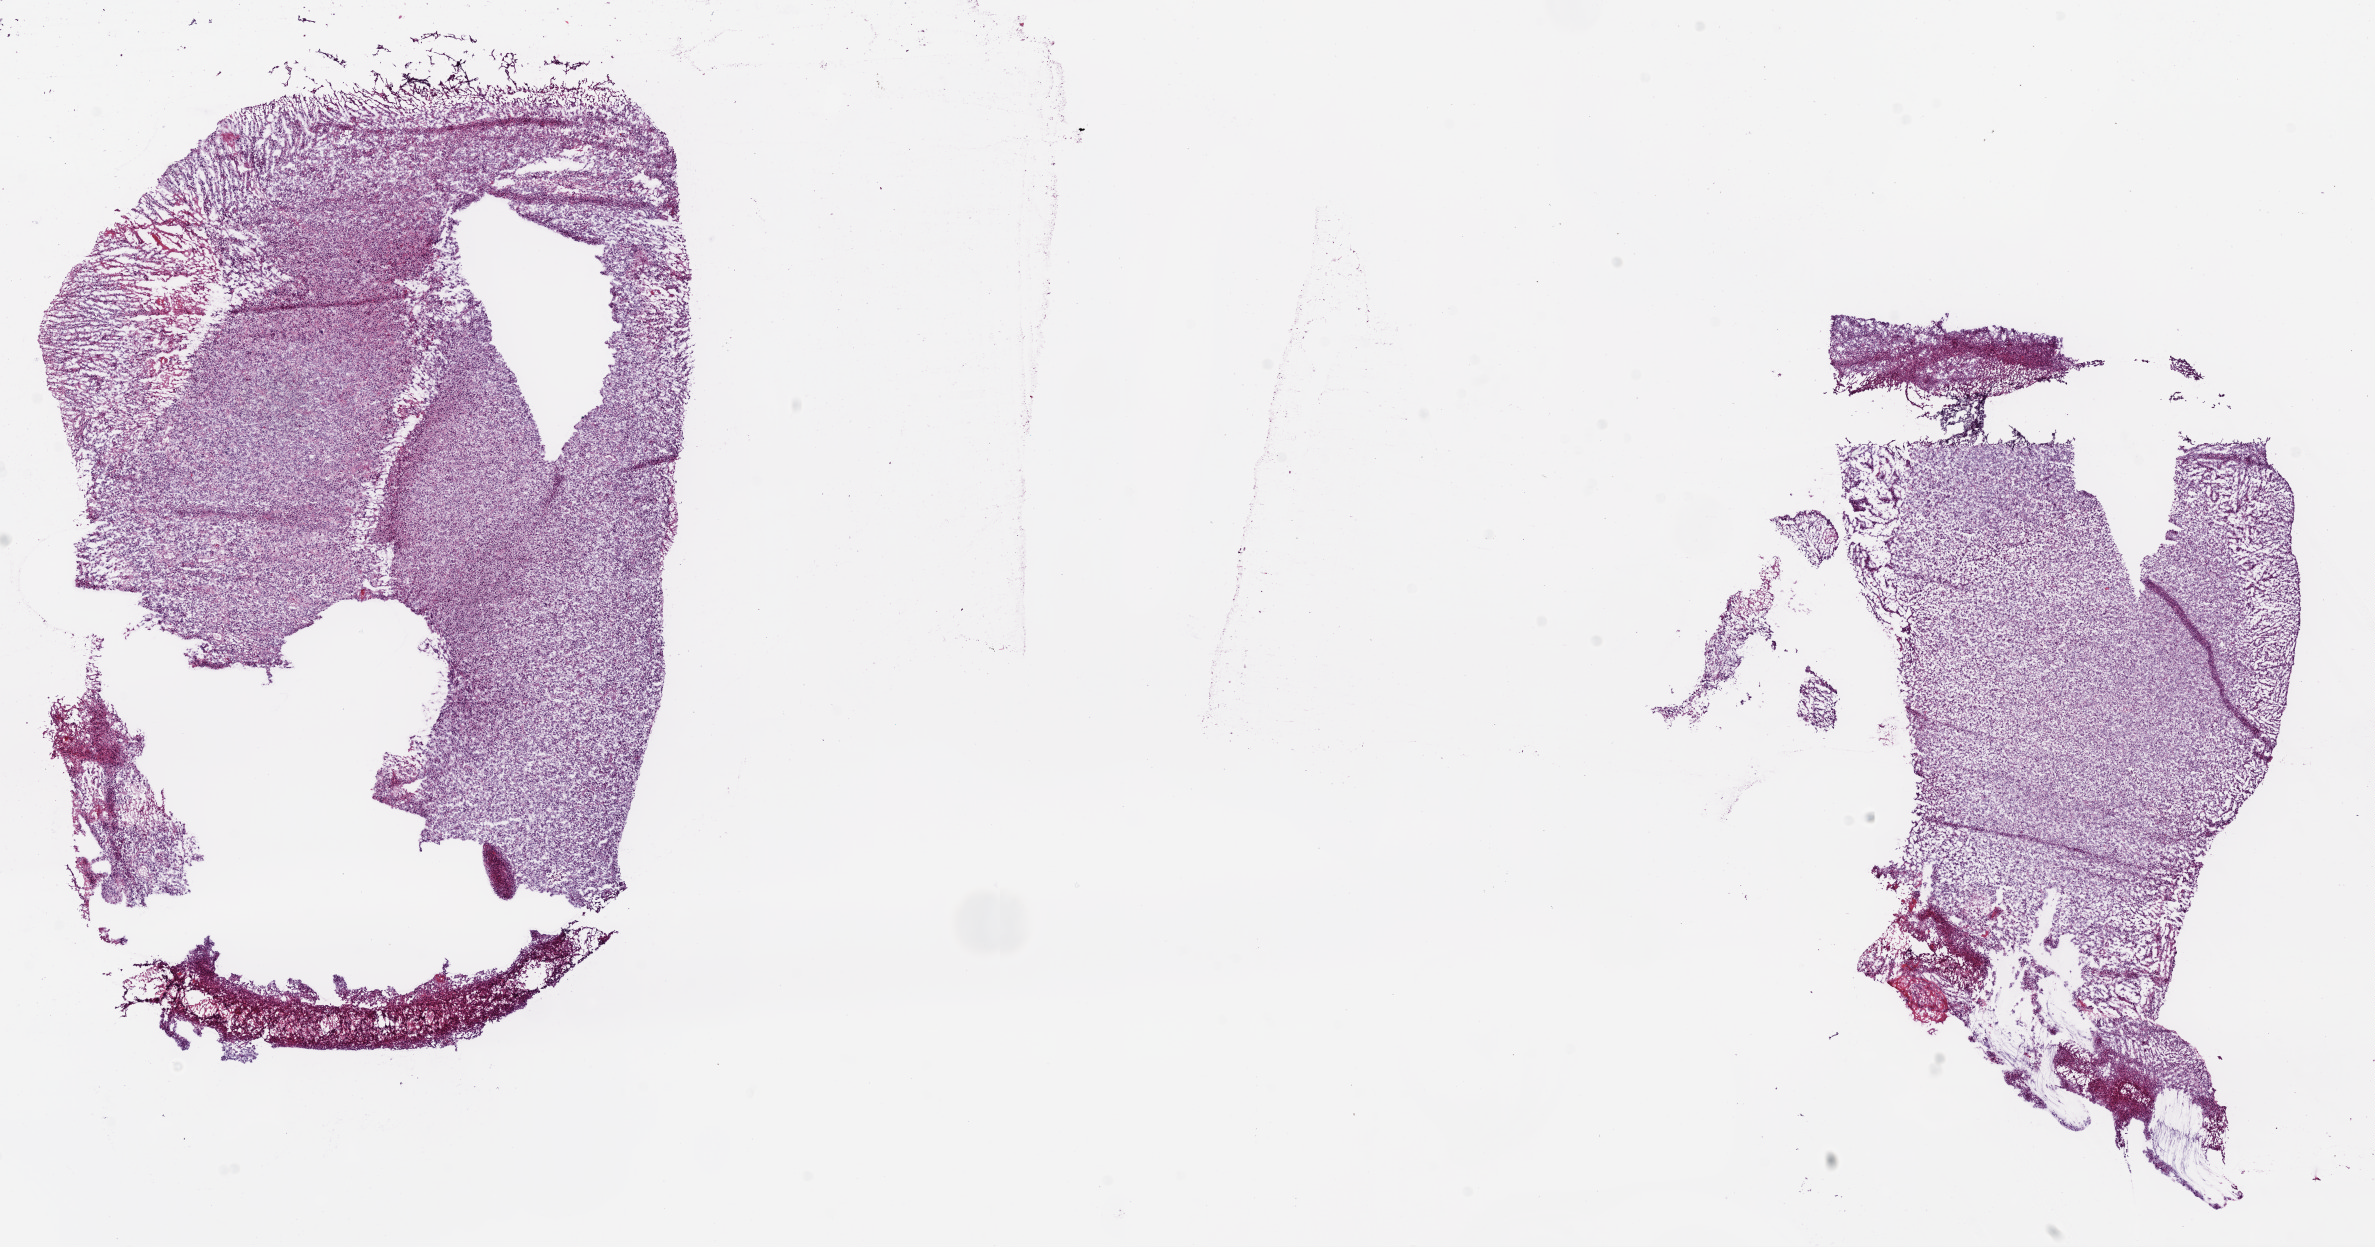
H&E-stained whole-slide image — low-resolution overview of the scanned area, about 19.1 x 10.0 mm. Frozen section from the bottom of the tissue portion. Brain, primary tumour sample. Female patient; age at initial diagnosis 38 years. Slide review estimates, as recorded: tumour nuclei 85%, normal cells 0%, stromal cells 0%, necrosis 20%.
* pathologic diagnosis: Glioblastoma